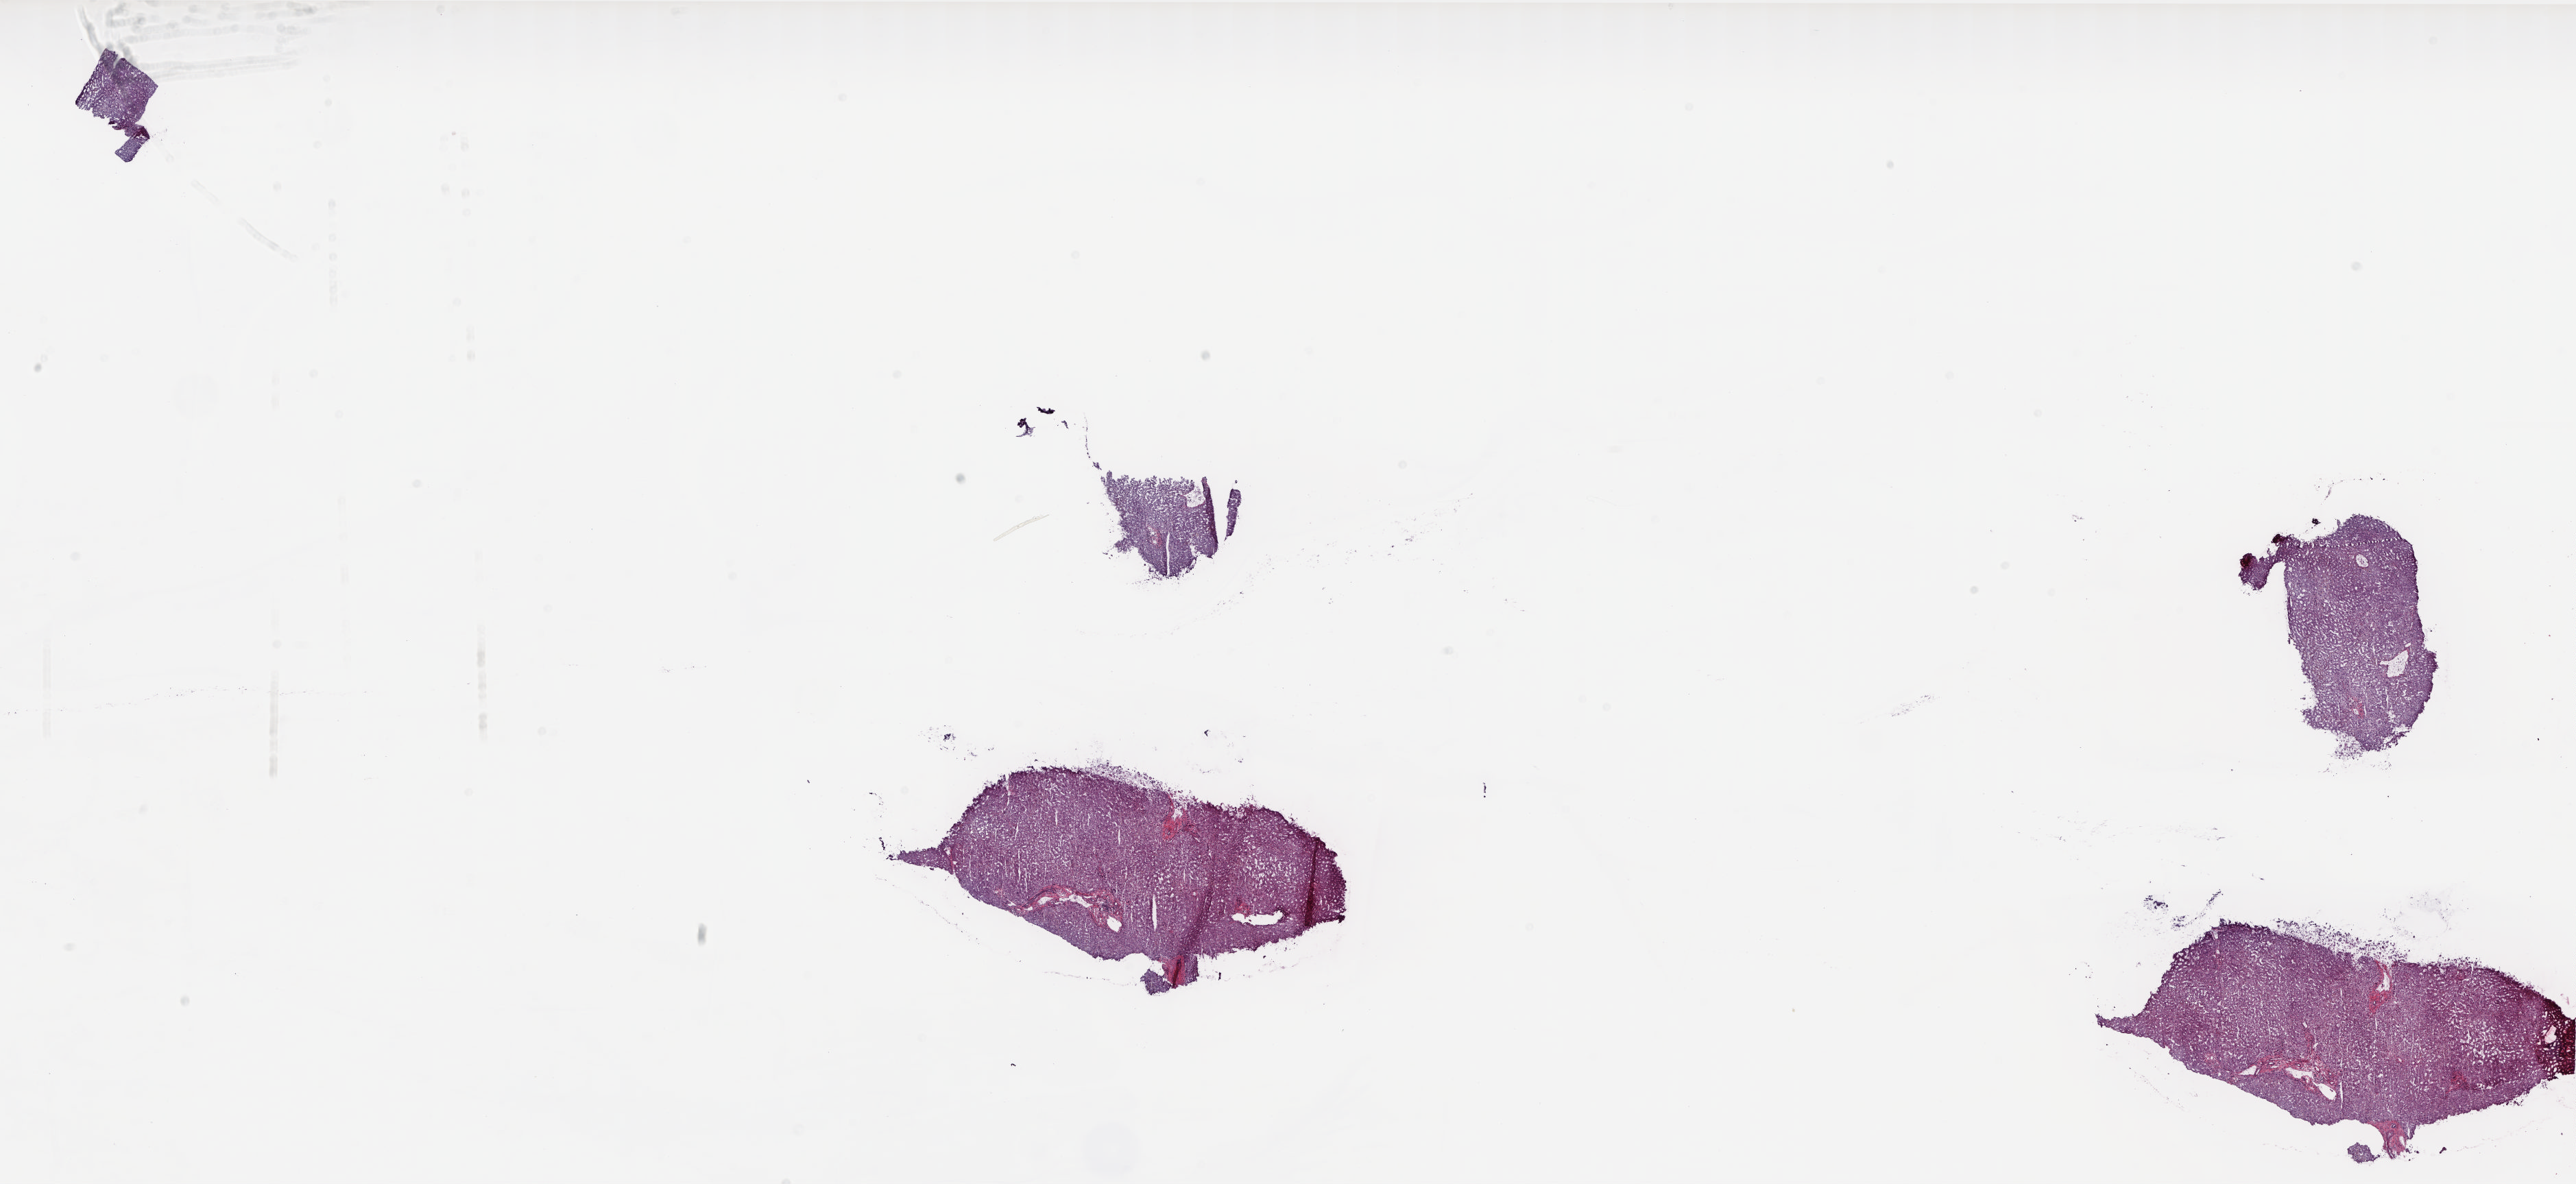
H&E whole-slide image — low-resolution overview of the scanned area, about 30.3 x 13.9 mm, frozen section from the top of the tissue portion, sample: solid tissue normal (non-tumour tissue), liver. Female patient; age at initial diagnosis 75 years. Slide review estimates, as recorded: tumour cells 0%, tumour nuclei 0%, normal cells 80%, stromal cells 20%, necrosis 0%. Infiltration values recorded for this section: lymphocyte infiltration 3%, monocyte infiltration 1%, neutrophil infiltration 2%.
• this section: solid tissue normal (non-tumour) sample from the same patient
• patient diagnosis: Hepatocellular carcinoma, NOS